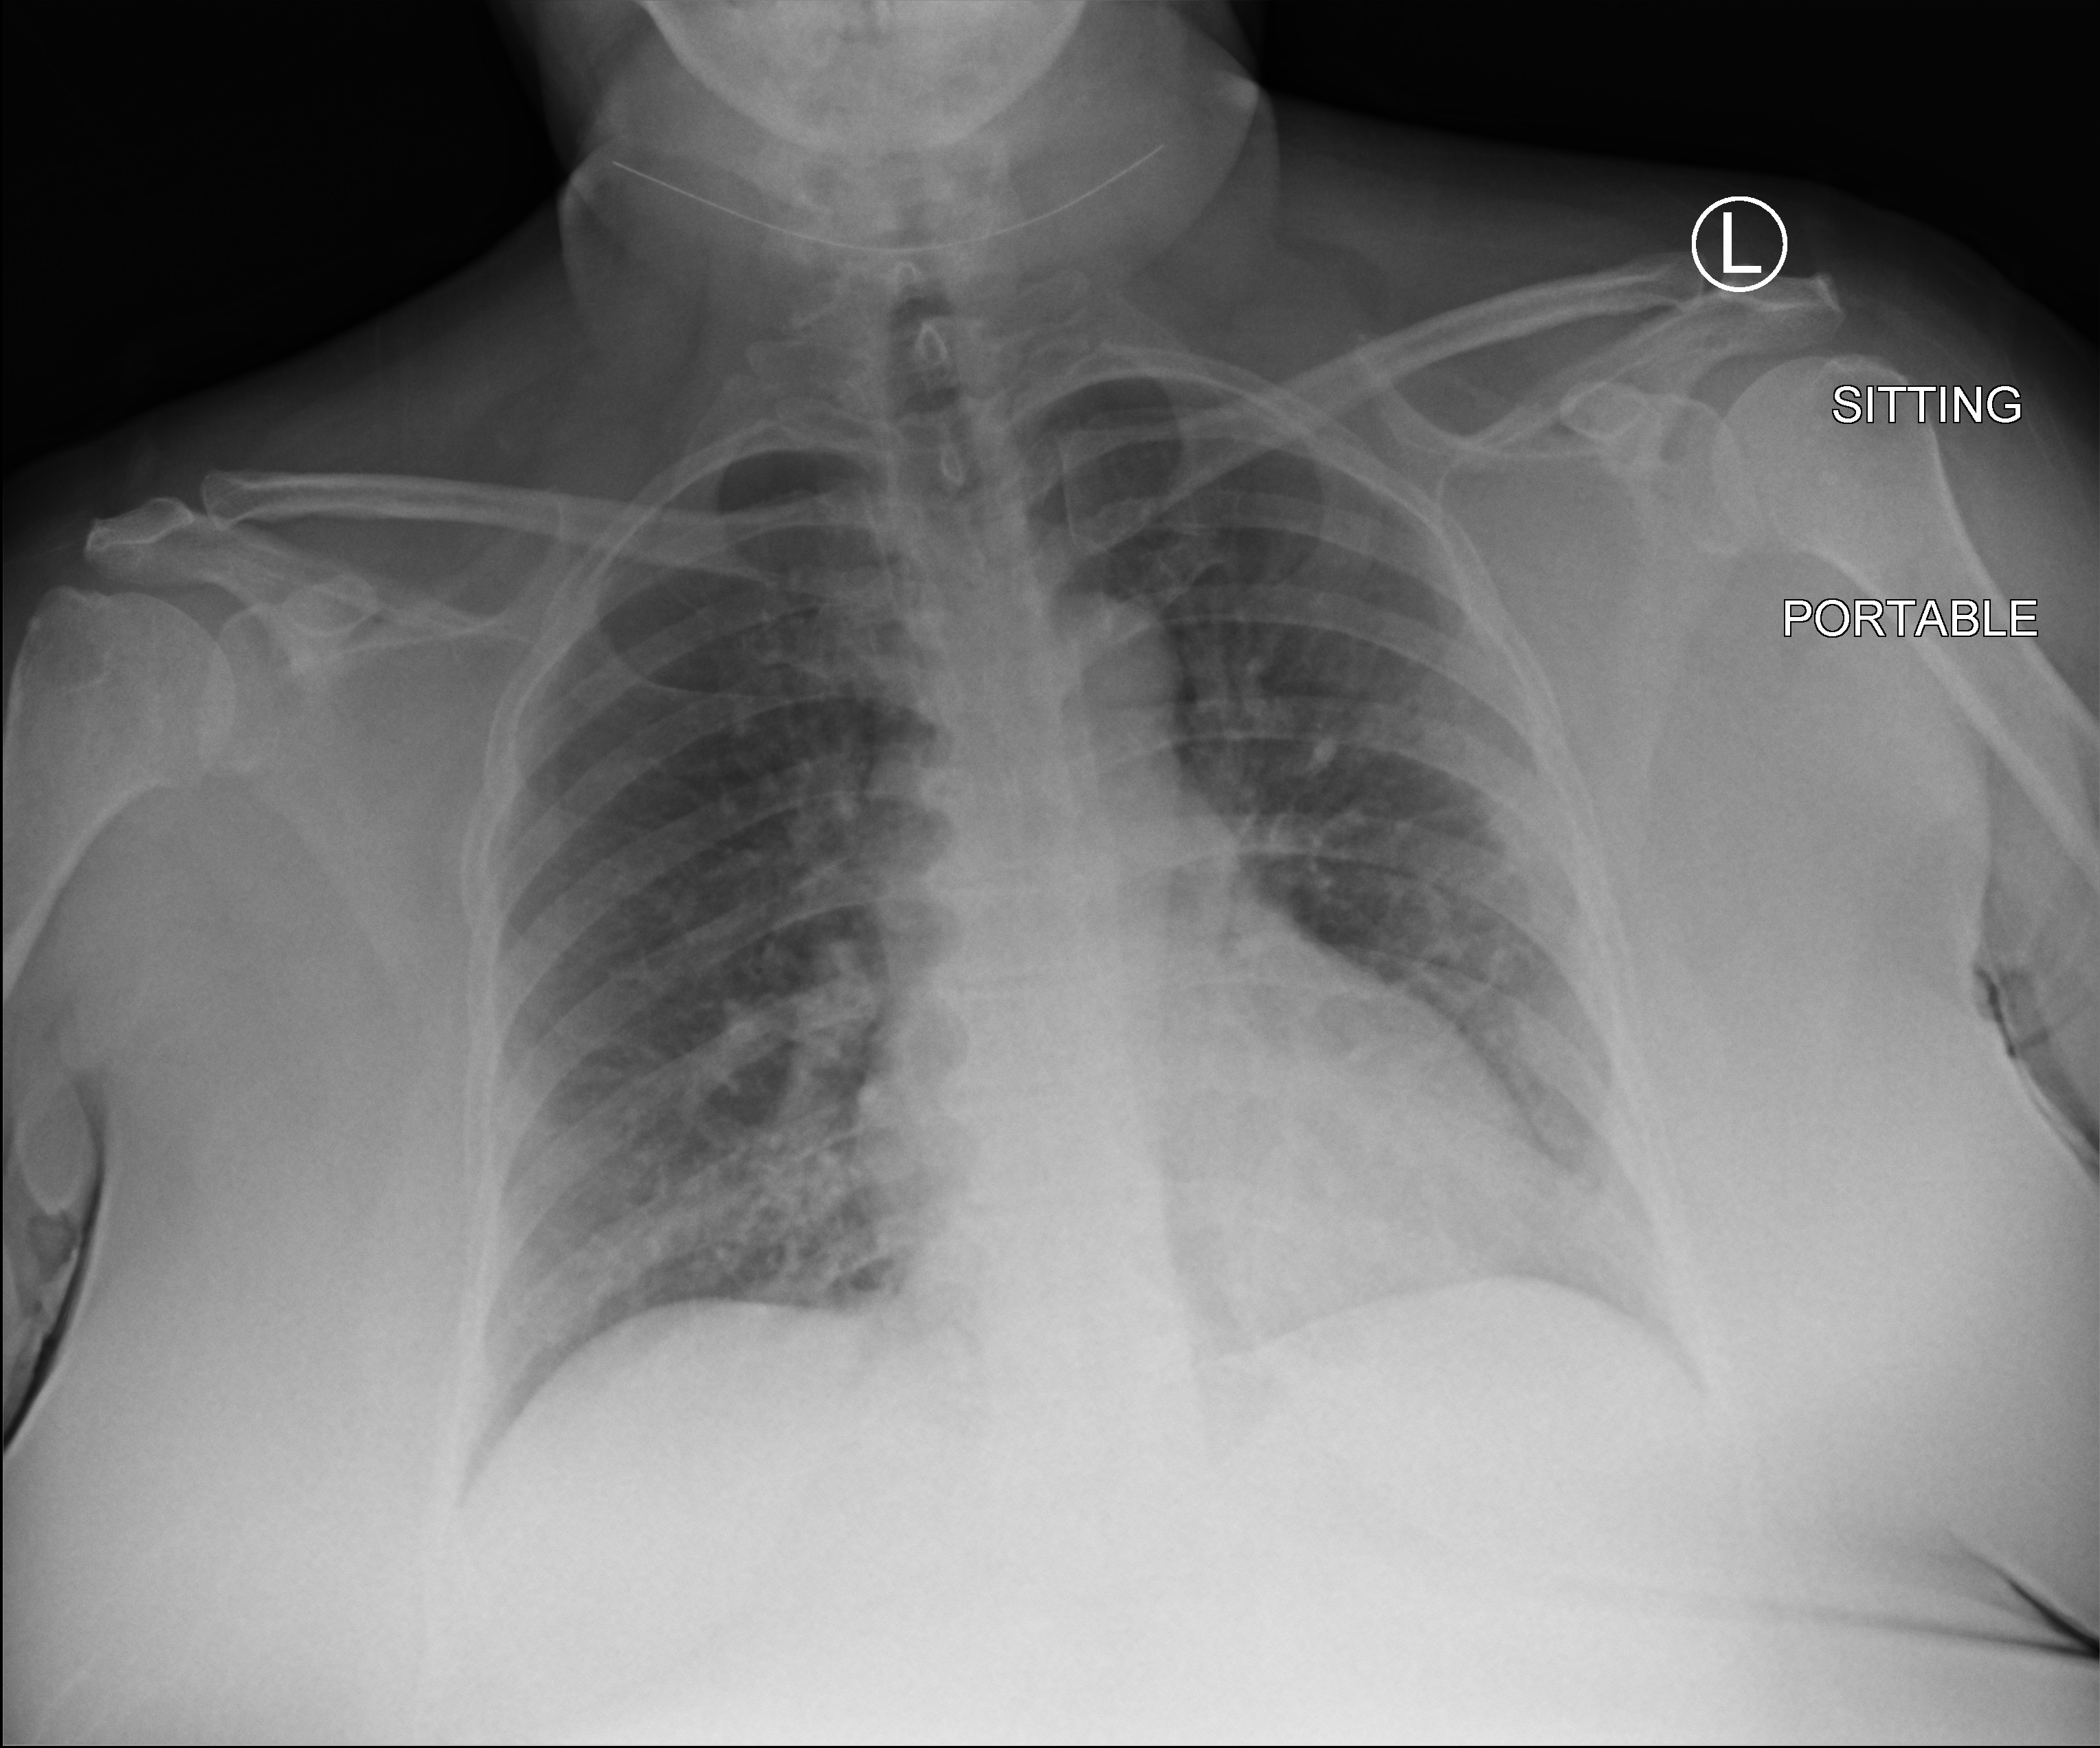
Chest X-ray (portable). Patient hospitalised with COVID-19; female, aged 18–59 years.
Admission-level facts for this patient (not findings on this image; timing relative to this image not recorded): mechanically ventilated during this hospital stay: no.